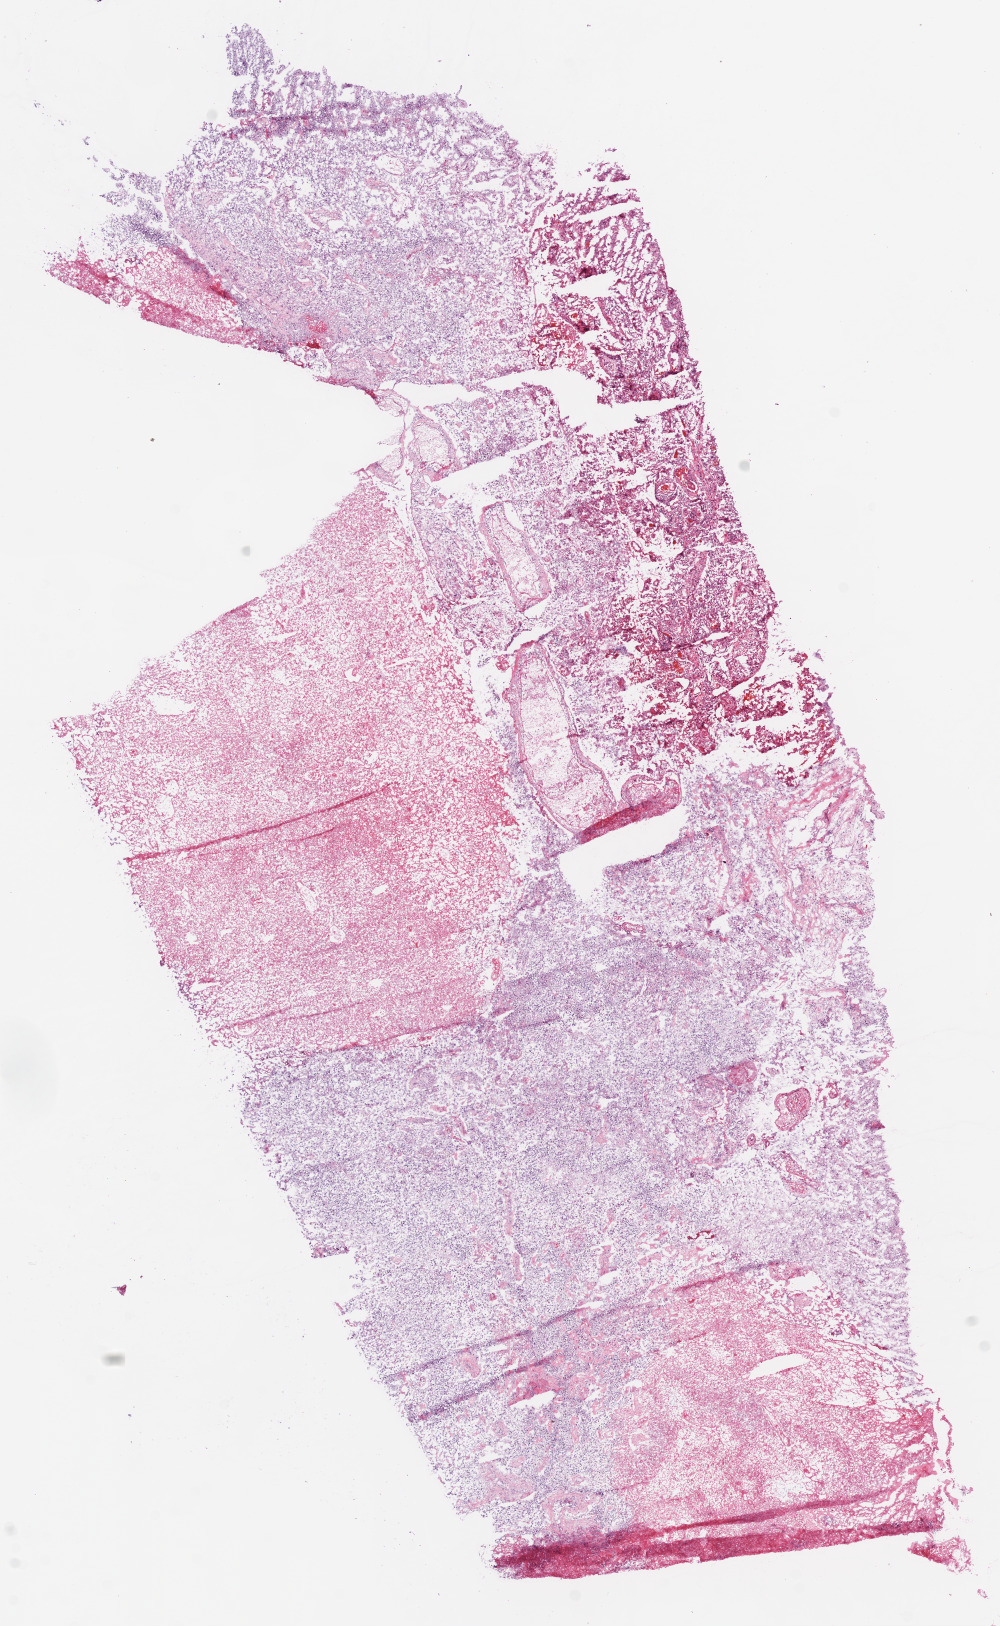
H&E-stained whole-slide image — whole scanned area (about 8.0 x 13.0 mm) shown as a low-resolution overview; frozen section from the bottom of the tissue portion; primary tumour sample from the brain. Male patient; age at initial diagnosis 68 years. Pathologist review of this section (percent, as recorded): tumour cells 60%, tumour nuclei 85%, normal cells 0%, stromal cells 0%, necrosis 40%.
• diagnosis: Glioblastoma (temporal lobe)